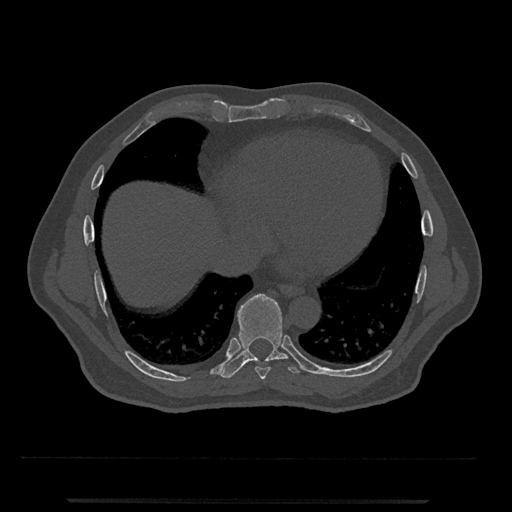
CT including the spine, one axial slice; slice 593 of 797 in the series (ordered by position); reconstruction kernel Br40s/3; 120 kVp; bone window (W 1800 / L 400 HU); 0.5 mm slice thickness; 512 × 512 image matrix, field of view 419 × 419 mm. Patient: male, 63 years. From the clinical record (not read from this slice): primary cancer: prostate.
Annotated regions visible in this slice (semi-automatic segmentation, software-assisted and operator-edited):
- T8 vertebra: box from (x=255, y=366) to (x=270, y=380) px
- T9 vertebra: (x=220, y=294)–(x=302, y=379)